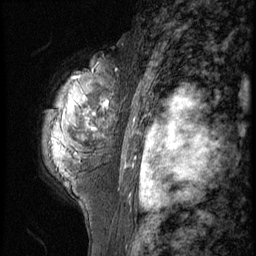
Breast MRI (dynamic contrast-enhanced), one sagittal slice. Position 40 of 56 along the scan axis. 3 images stored at this slice position (order not interpretable as contrast timing). 1.5 T. TE 4.2 ms, TR 9 ms. 2.5 mm slice thickness. 256 × 256 image matrix, field of view 180 × 180 mm. Female patient, age 50 years. Case-level facts recorded for this patient, not image findings: setting: breast cancer imaged before/during neoadjuvant chemotherapy; receptor status: triple-negative.
Annotated regions visible in this slice (semi-automatic segmentation, software-assisted and operator-edited):
- analysis volume of interest (the breast-tissue region the enhancement analysis was run in; not a lesion): bounding box [x1, y1, x2, y2] px = [41, 53, 126, 191]
- tumour enhancement mask (voxels above the 140 % enhancement threshold inside the analysis volume of interest): [83, 98, 106, 130]